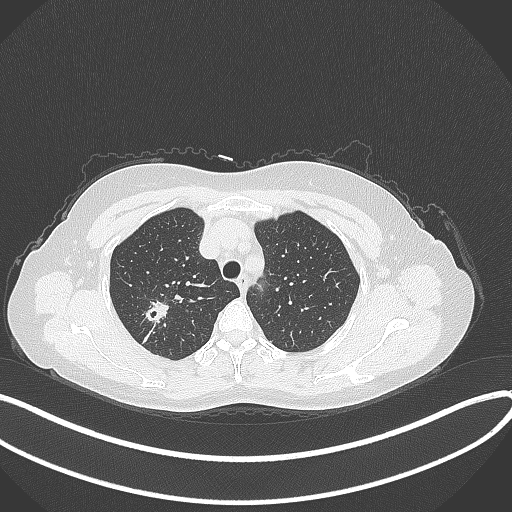
Chest CT, one axial slice; slice 289 of 337 in the series (ordered by position); reconstruction kernel B70f; lung window (W 1500 / L -600 HU); 512 × 512 image matrix. Female patient, age 50 years. Case-level facts recorded for this patient, not image findings: clinical TNM (as recorded): T1c N0 M0; histopathological grade: G2-3.
Annotated regions visible in this slice (rectangle marked by the reading radiologist):
- lung tumour (recorded histology: adenocarcinoma): bounding box <139,298,175,328> (left, top, right, bottom; pixels)